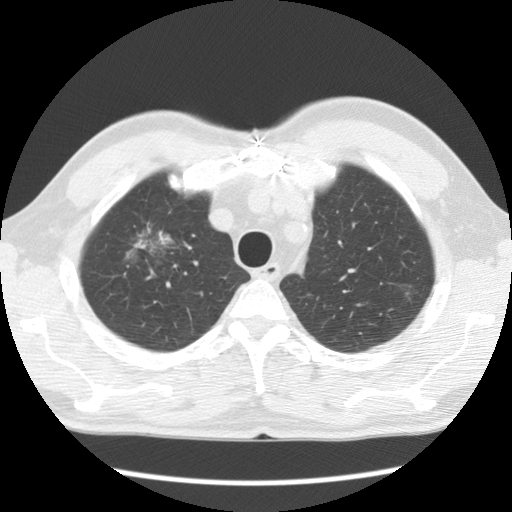
Low-dose screening chest CT, axial slice, first (baseline) screen, lung window (W 1500 / L -600 HU), slice 22 of 132 in the series. Male participant, aged 64 years at enrolment.
- Expert-annotated lung lesion, bounding box [x1, y1, x2, y2] px = [98, 199, 177, 276].
- The screening reader recorded 2 non-calcified nodules or masses ≥4 mm on this exam (right upper lobe, left upper lobe); which of them this box marks is not recorded.
- Official screen result: positive, change unspecified: nodule(s) >= 4 mm or enlarging nodule(s), mass(es), or other non-specific abnormalities suspicious for lung cancer.
- Later outcome: lung cancer diagnosed 750 days after this screen (after the third annual screen) — adenocarcinoma, NOS, right upper lobe, well differentiated (G1), stage IB (AJCC 6th edition), 45 mm at pathology.